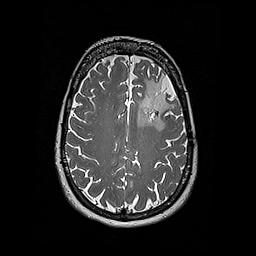
Brain MRI from a brain-tumour surgery series, one axial slice; position 127 of 192 along the scan axis; 1 mm slice thickness; 256 × 256 image matrix. From the clinical record (not read from this slice): histopathology: Oligodendroglioma; WHO grade: 2; IDH mutation: yes.
Structures marked on this image (manually delineated by an expert):
- tumour: bounding box (x1, y1, x2, y2) in pixels: (137, 78, 159, 127)